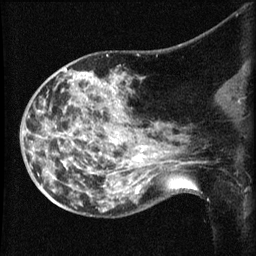
Breast MRI (dynamic contrast-enhanced), one sagittal slice. Slice 31 of 60 in the series (ordered by position). Dynamic contrast-enhanced series, image 2 of 3 at this slice position (ordered by acquisition). 1.5 T. TE 4.2 ms, TR 8.2 ms. 256 × 256 image matrix, field of view 180 × 180 mm. Female patient, age 50 years.
Structures marked on this image (semi-automatic segmentation, software-assisted and operator-edited):
- analysis volume of interest (the breast-tissue region the enhancement analysis was run in; not a lesion): bounding box (x1, y1, x2, y2) in pixels: (38, 73, 169, 211)
- tumour enhancement mask (voxels above the 70 % enhancement threshold inside the analysis volume of interest): (136, 149, 144, 161)